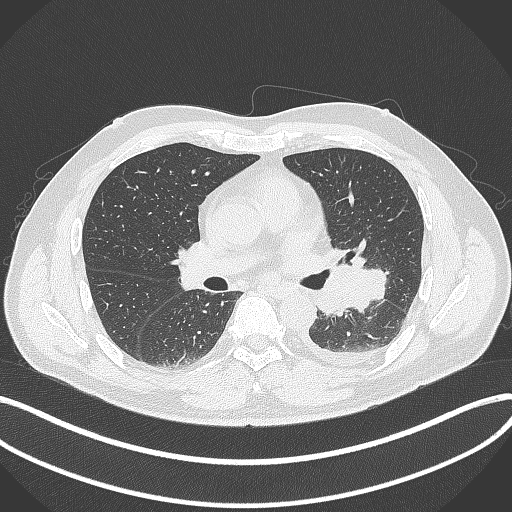
Chest CT, one axial slice; slice 197 of 342 in the series (ordered by position); reconstruction kernel B70f; 120 kVp; lung window (W 1500 / L -600 HU); 512 × 512 image matrix, field of view 400 × 400 mm. Patient: male, 58 years. Case-level facts recorded for this patient, not image findings: clinical TNM (as recorded): T3 N1 M1b; histopathological grade: G3.
Outlined on this slice (rectangle marked by the reading radiologist):
- lung tumour (recorded histology: small cell carcinoma): box from (x=314, y=263) to (x=390, y=322) px